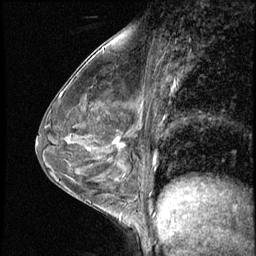
Breast MRI (dynamic contrast-enhanced), one sagittal slice. Slice 34 of 56 in the series (ordered by position). 3 images stored at this slice position (order not interpretable as contrast timing). 1.5 T. TE 4.2 ms, TR 8.7 ms. 2.5 mm slice thickness. 256 × 256 image matrix. Patient: female, 43 years. From the clinical record (not read from this slice): setting: breast cancer imaged before/during neoadjuvant chemotherapy; receptor status: HR-positive, HER2-negative.
Structures marked on this image (semi-automatic segmentation, software-assisted and operator-edited):
- analysis volume of interest (the breast-tissue region the enhancement analysis was run in; not a lesion): bounding box <101,120,145,165> (left, top, right, bottom; pixels)
- tumour enhancement mask (voxels above the 140 % enhancement threshold inside the analysis volume of interest): <113,137,125,149>